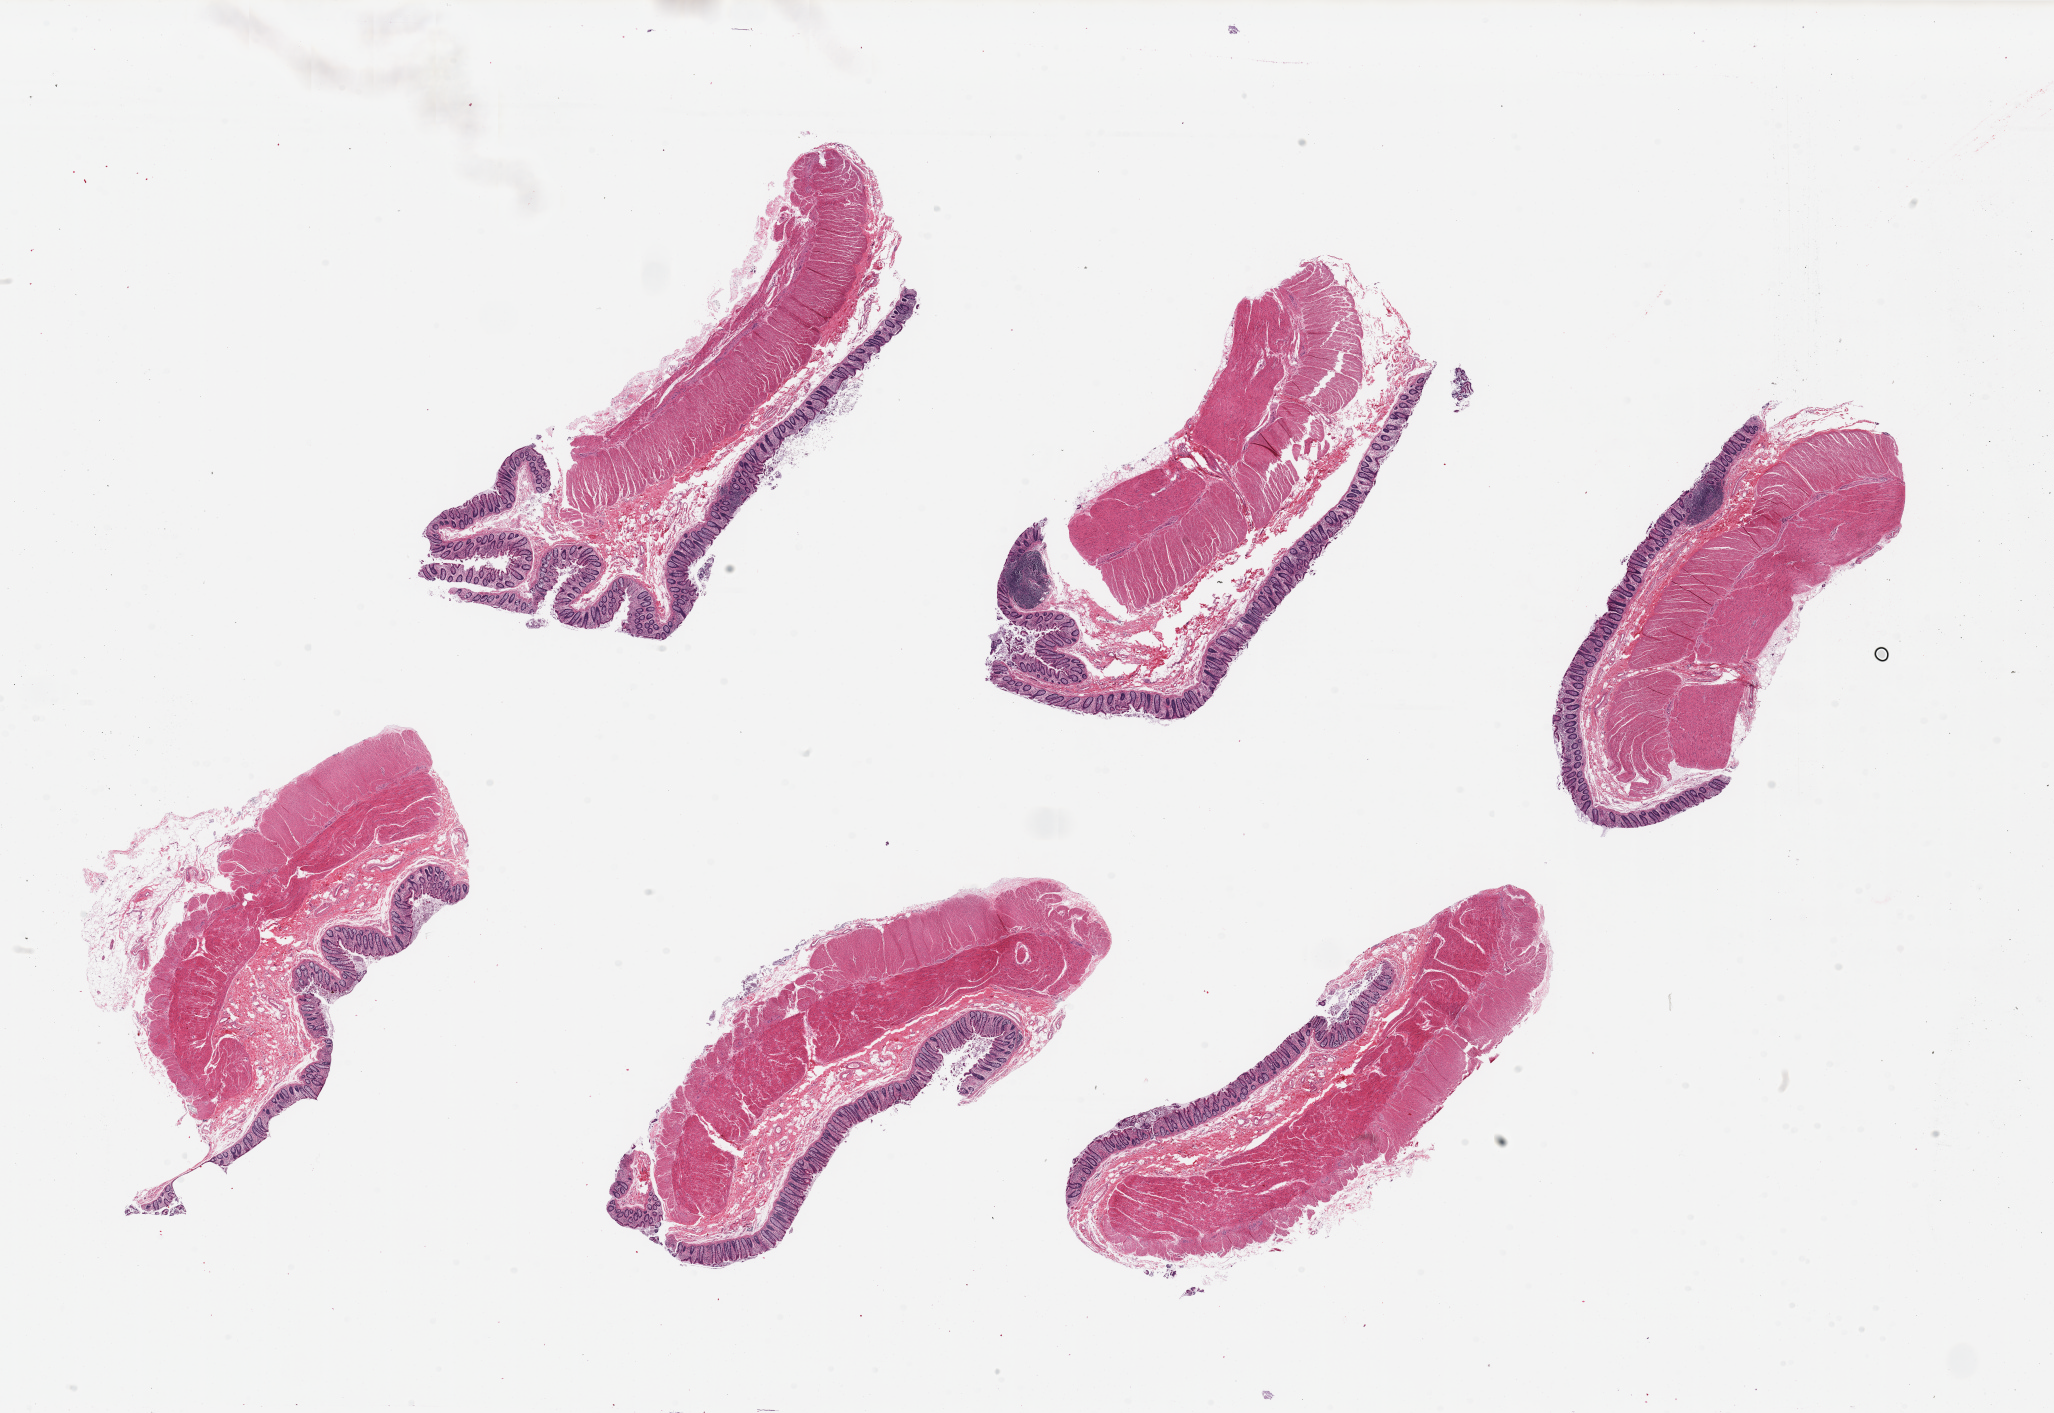
Digitized haematoxylin and eosin-stained section, shown as a low-resolution overview of the whole scanned area (about 32.5 x 22.3 mm); PAXgene-fixed, paraffin-embedded tissue; sampled site (target tissue): transverse colon; donor tissue sample. Female donor.
* review note (as recorded): 6 pieces, up to 9.5x4mm; ~mucsoa well preserved, ~10% thickness